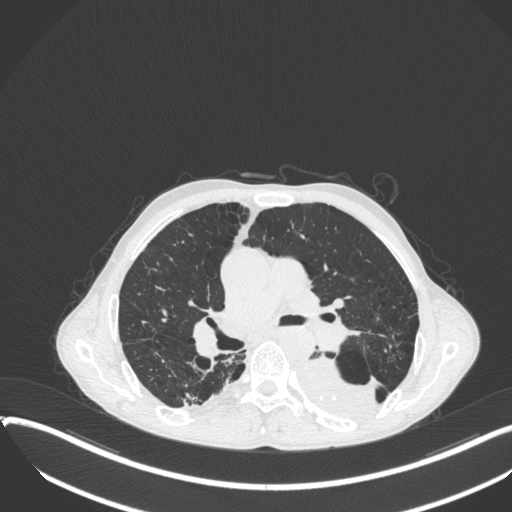
Chest CT, one axial slice. Position 225 of 400 along the scan axis. Reconstruction kernel B31f. Lung window (W 1500 / L -600 HU). 512 × 512 image matrix, field of view 400 × 400 mm. Patient: male, 57 years. Case-level facts recorded for this patient, not image findings: clinical TNM (as recorded): T4 N0 M0.
Annotated regions visible in this slice (bounding box drawn by a radiologist):
- lung tumour (recorded histology: squamous cell carcinoma): bounding box <290,343,385,427> (left, top, right, bottom; pixels)